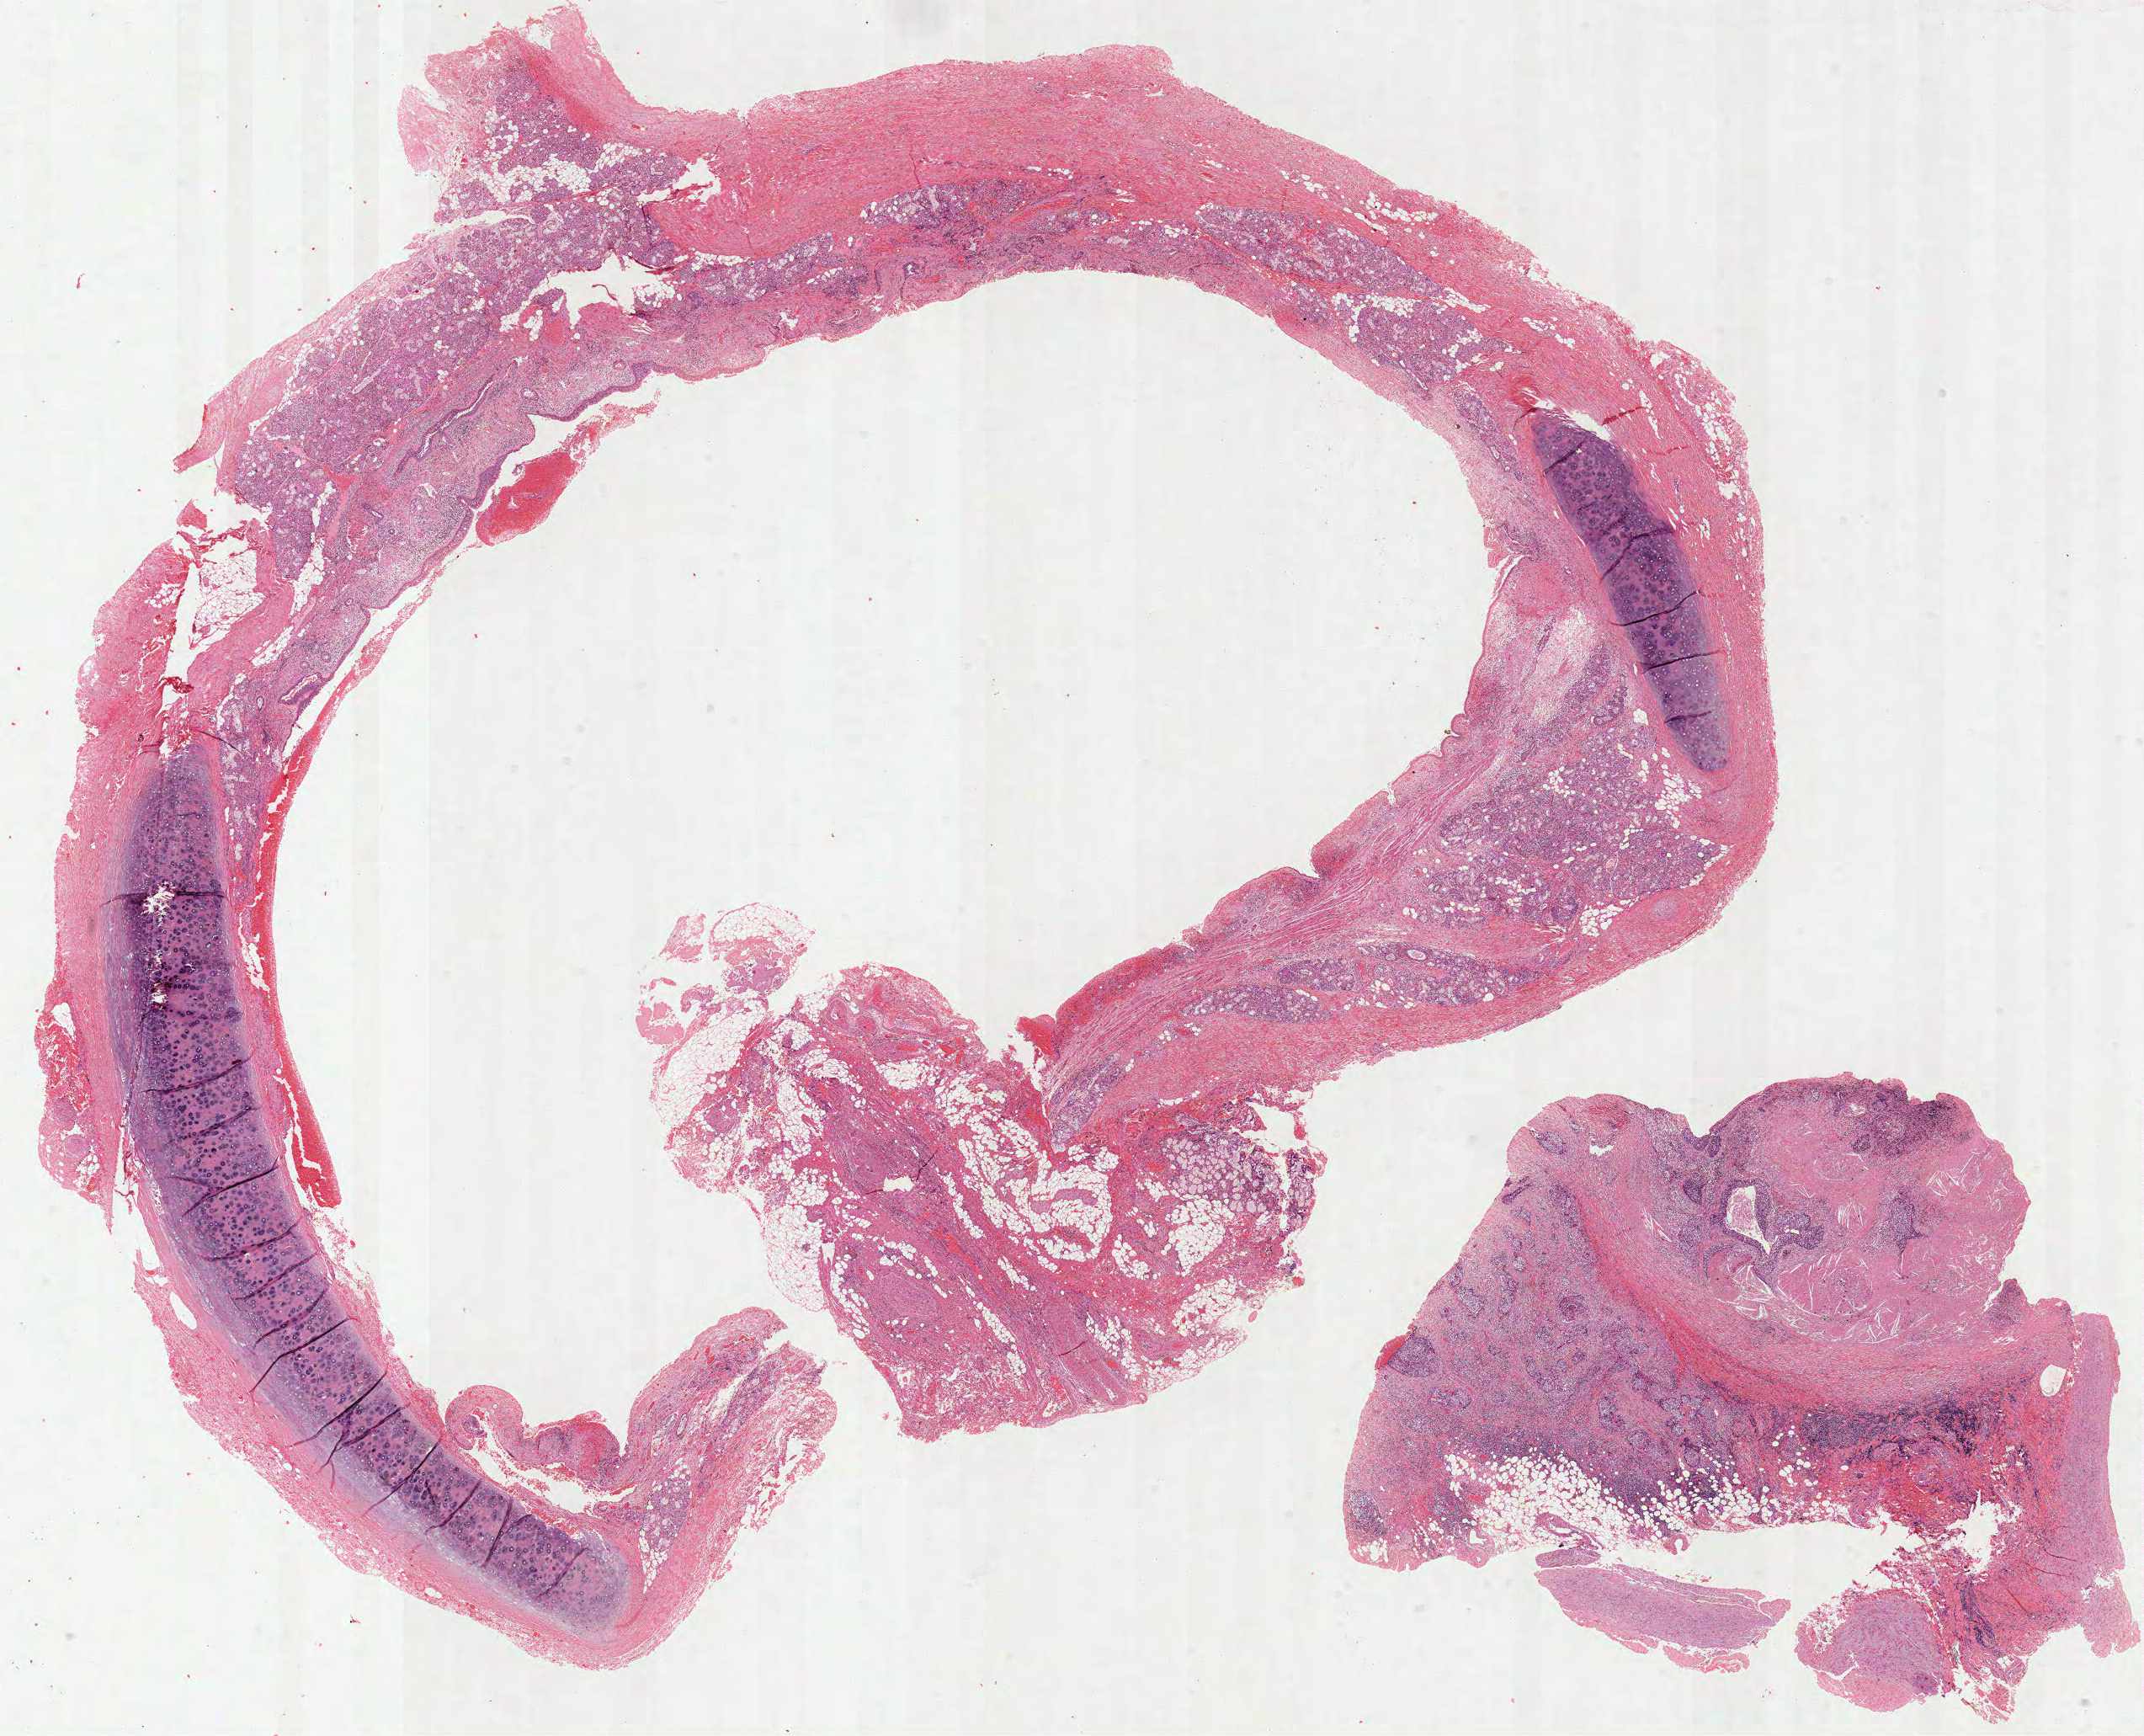
H&E whole-slide image, low-resolution overview of the scanned area, about 20.5 x 16.6 mm (from a 40x scan). Formalin-fixed paraffin-embedded (FFPE) diagnostic section. Lung, primary tumour sample. Male patient; age at initial diagnosis 74 years.
AJCC pathologic stage: IIA (6th edition). TNM: T1 N1 M0. Pathologic diagnosis: Squamous cell carcinoma, NOS.